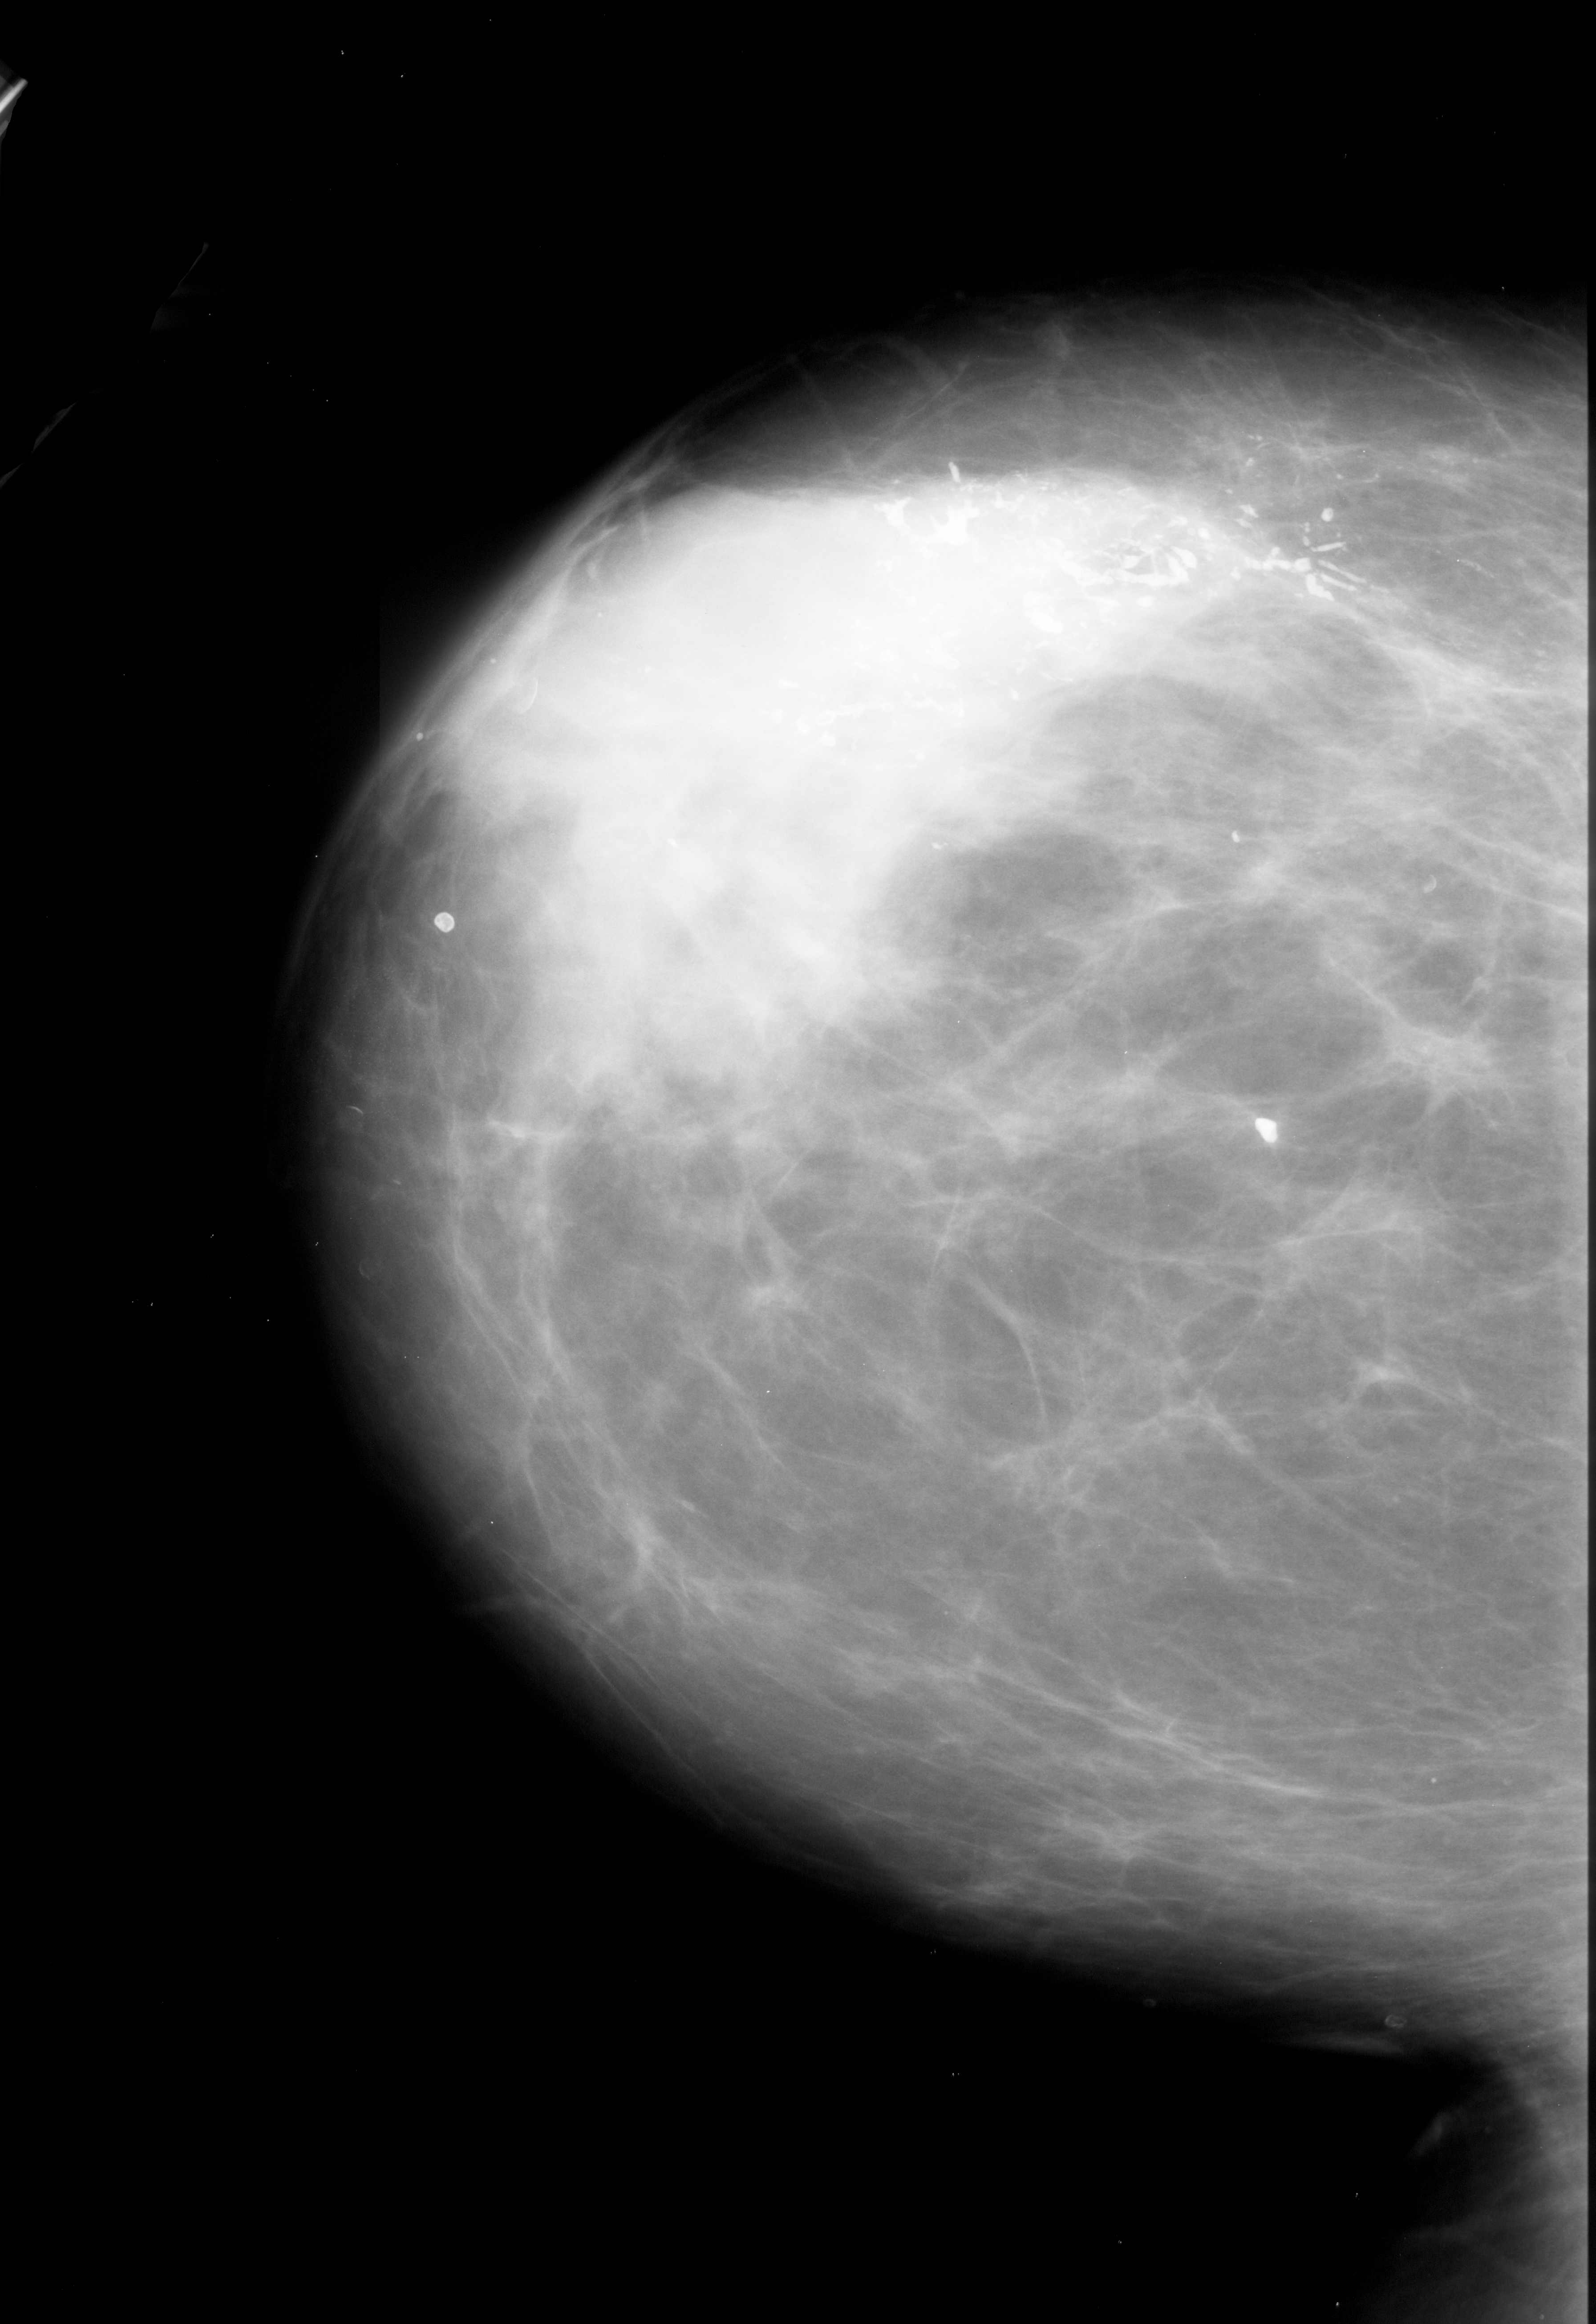
Scanned film-screen mammogram. Left breast. CC view. 1596 × 2324 image matrix.
Expert-marked regions of interest on this image (one box per marked abnormality):
- calcifications, morphology pleomorphic, distribution segmental; BI-RADS assessment category 5; subtlety rating 5 on a 1 (subtle) to 5 (obvious) scale; pathology (as recorded): malignant: bounding box [x1, y1, x2, y2] px = [410, 403, 1584, 919]